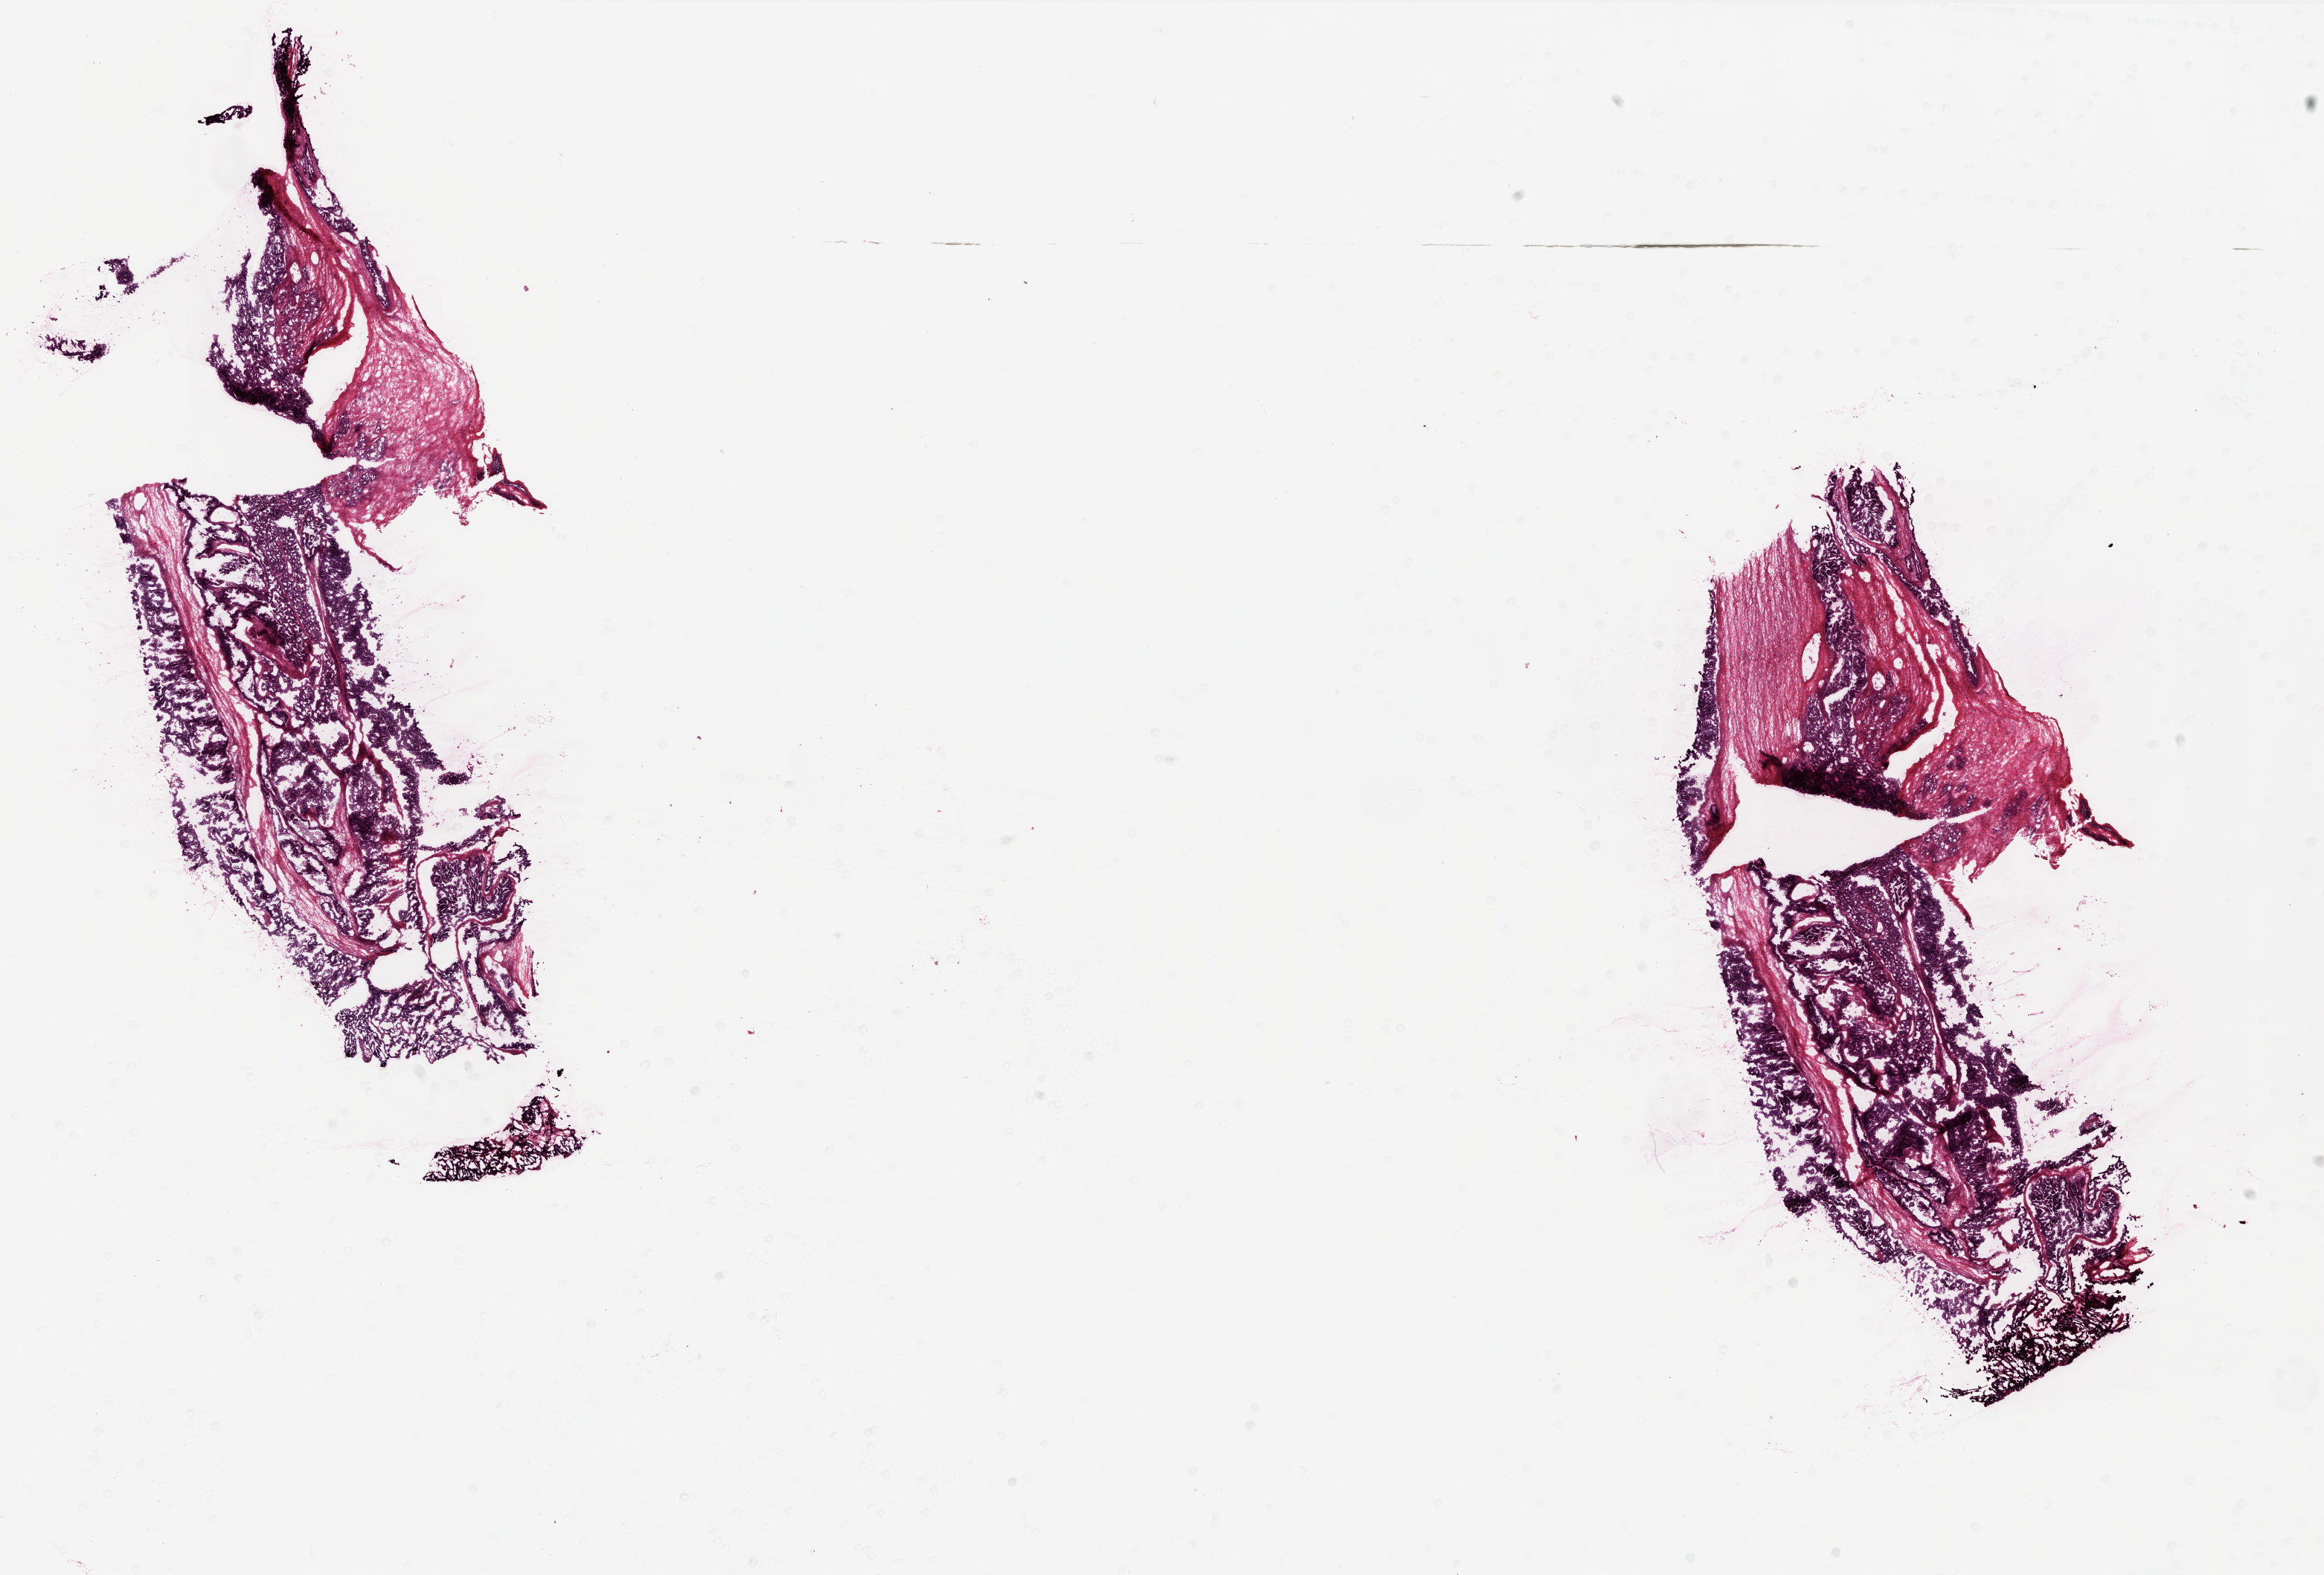
Hematoxylin and eosin (H&E) stained whole-slide image, shown as a low-resolution overview of the whole scanned area (about 25.0 x 16.9 mm, from a 20x scan); frozen section from the top of the tissue portion; ovary, primary tumour sample. Patient: female, age at initial diagnosis 47 years. Histologic grade: G3 (poorly differentiated). Pathologist review of this section (percent, as recorded): tumour cells 75%, tumour nuclei 85%, normal cells 0%, stromal cells 25%, necrosis 0%.
FIGO stage: IIIC. Diagnosis: Serous cystadenocarcinoma, NOS.